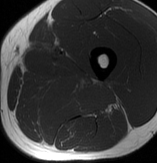
MRI of an extremity soft-tissue mass, one axial slice; slice 39 of 70 in the series (ordered by position); MR volume resampled by the dataset authors to the PET/CT grid (not the native acquisition matrix); 157 × 163 image matrix, field of view 153 × 159 mm. Male patient. From the clinical record (not read from this slice): histological type: extraskeletal osteosarcoma; grade: high; site of the primary tumour: left adductur.
Annotated regions visible in this slice (expert contour drawn on MRI and transferred to this co-registered scan by the dataset authors):
- gross tumour volume (mass): bounding box <15,71,123,120> (left, top, right, bottom; pixels)